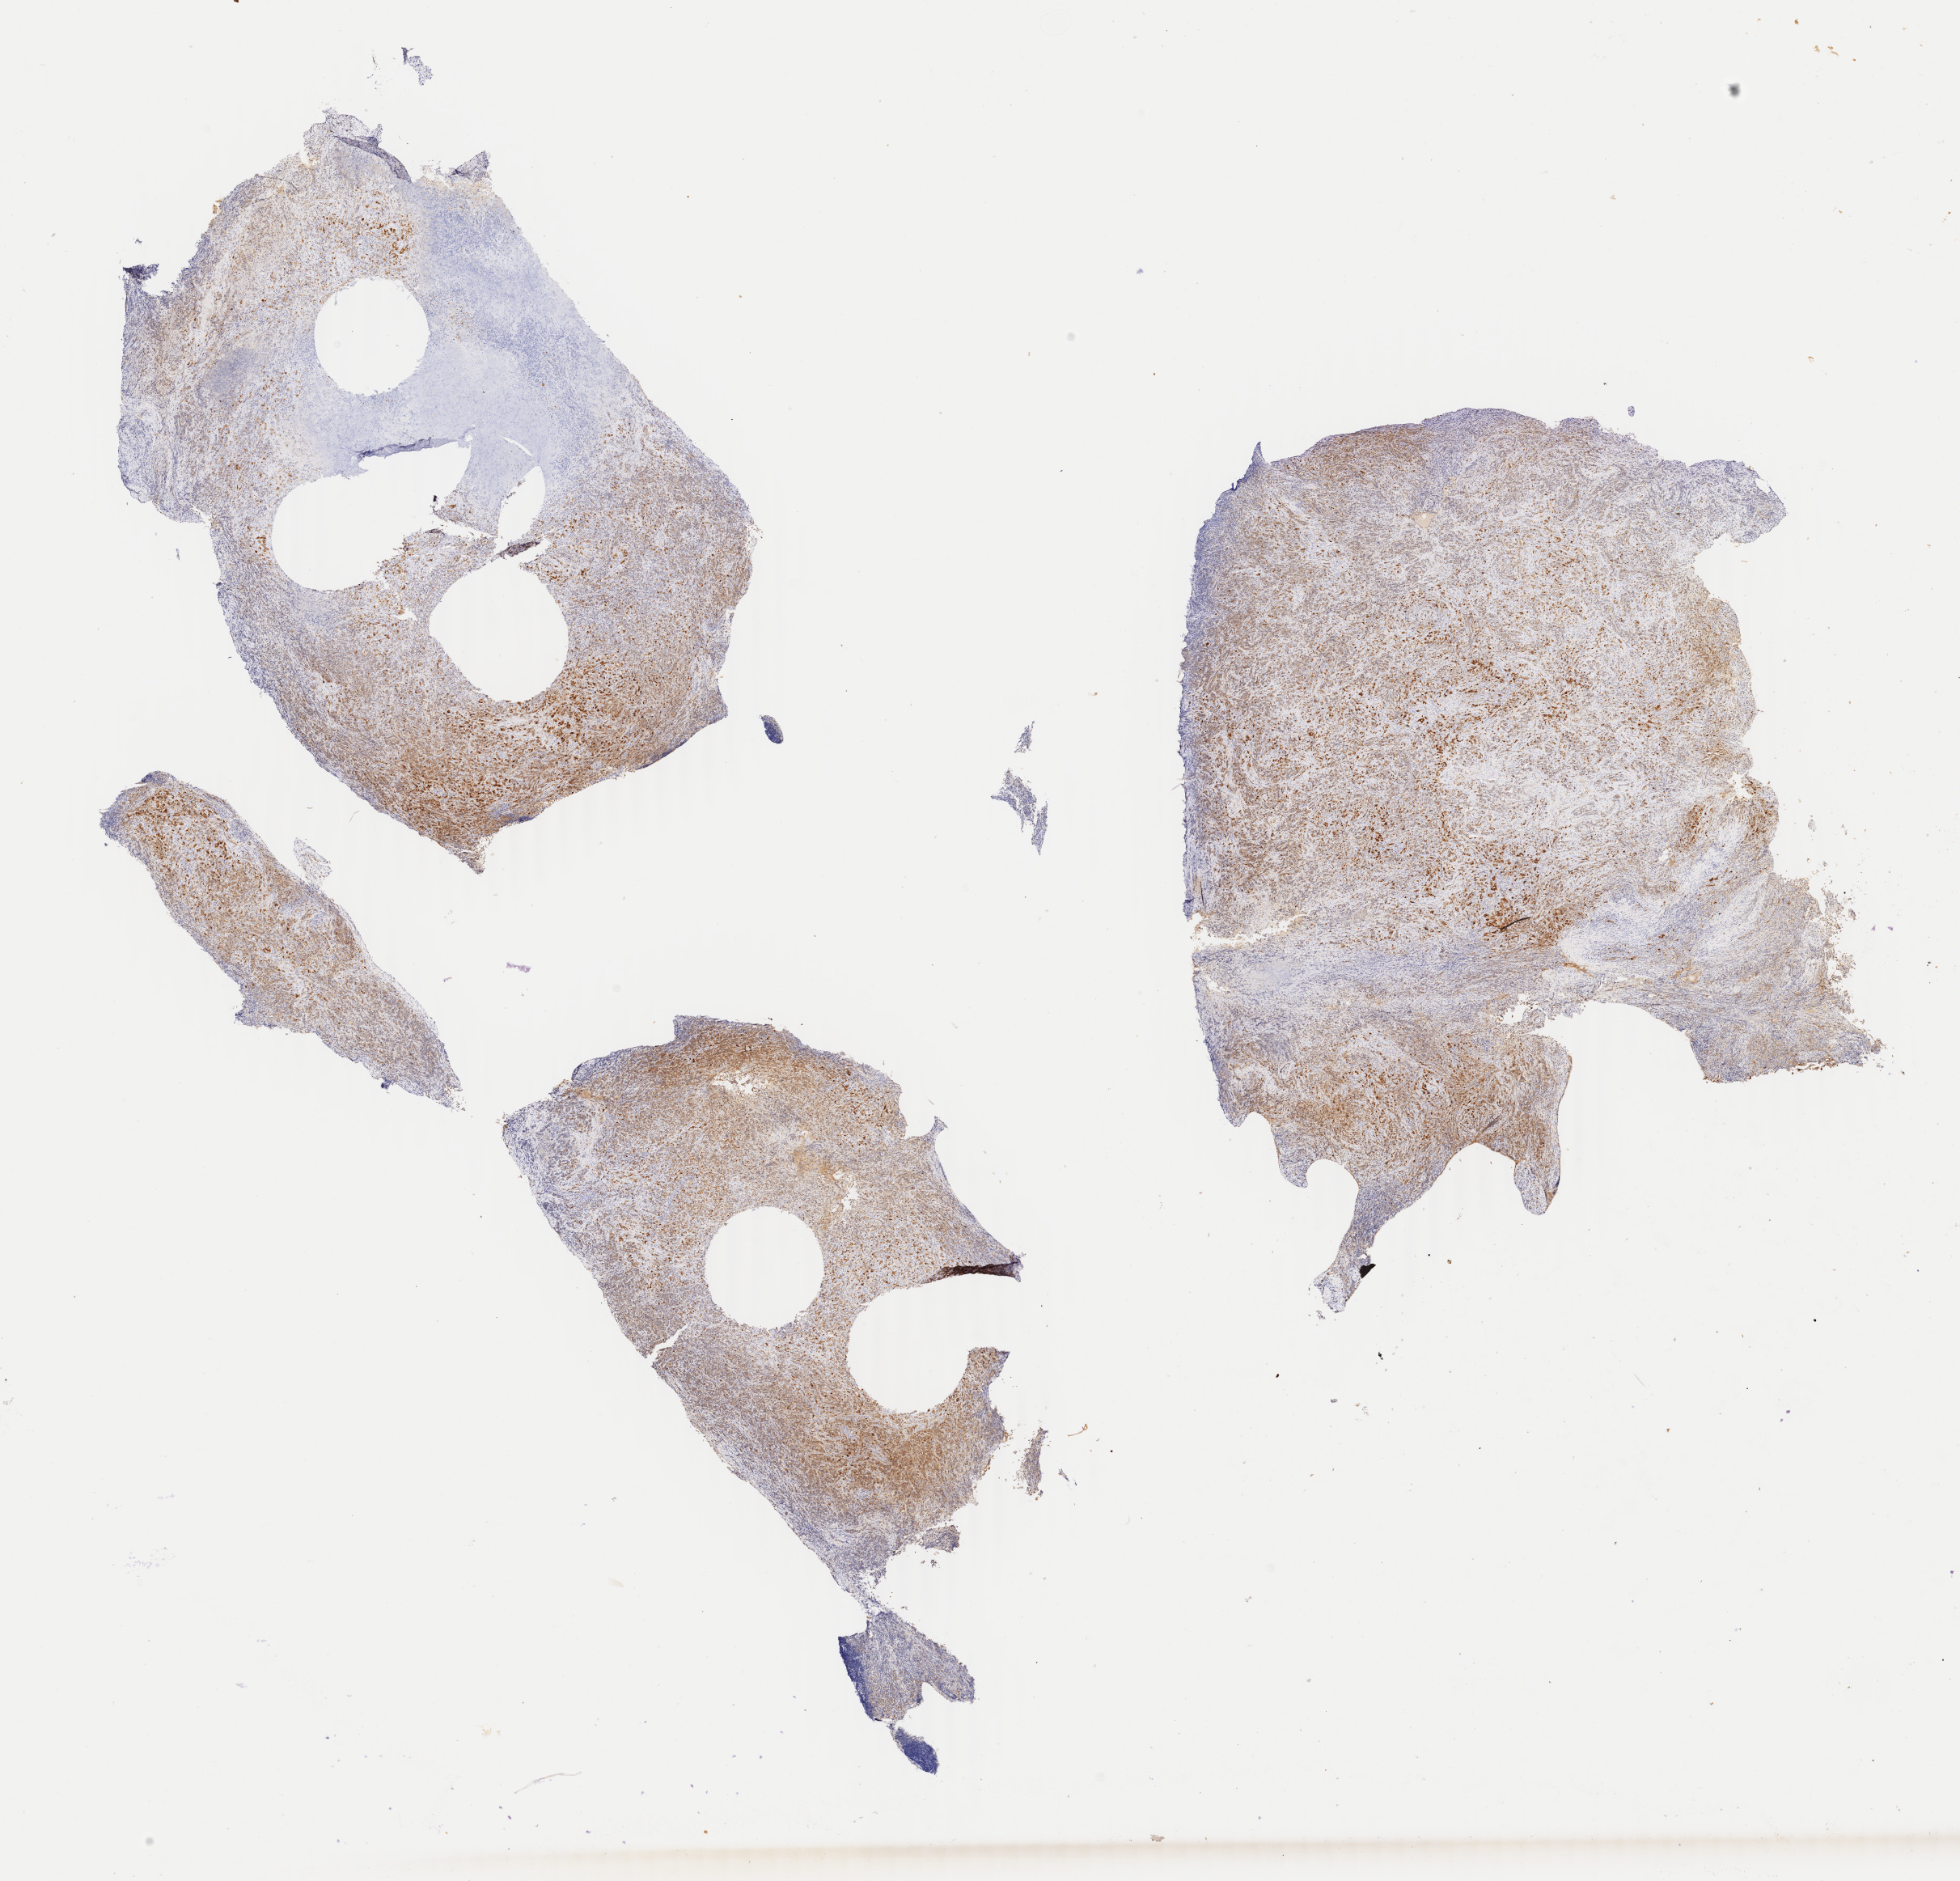
Immunohistochemistry (IHC) whole-slide image stained for p16 (p16INK4a) — a low-resolution overview of the entire scanned area, about 19.3 x 18.5 mm, specimen: tumor tissue, site: lung (left). Patient: male, aged 65.
Histologic diagnosis: Carcinoma, undifferentiated, NOS.